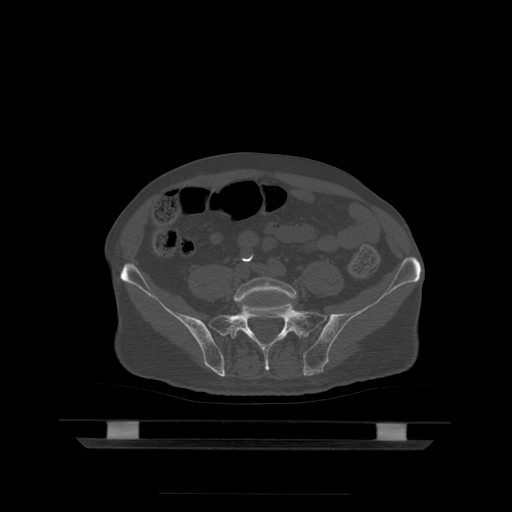
CT including the spine, one axial slice; slice 60 of 522 in the series (ordered by position); bone window (W 1800 / L 400 HU); 1.25 mm slice thickness; 512 × 512 image matrix. Patient age 68 years. Case-level facts recorded for this patient, not image findings: primary cancer: urothelial.
Annotated regions visible in this slice (semi-automatically segmented with operator editing):
- L5 vertebra: box from (x=235, y=277) to (x=297, y=305) px